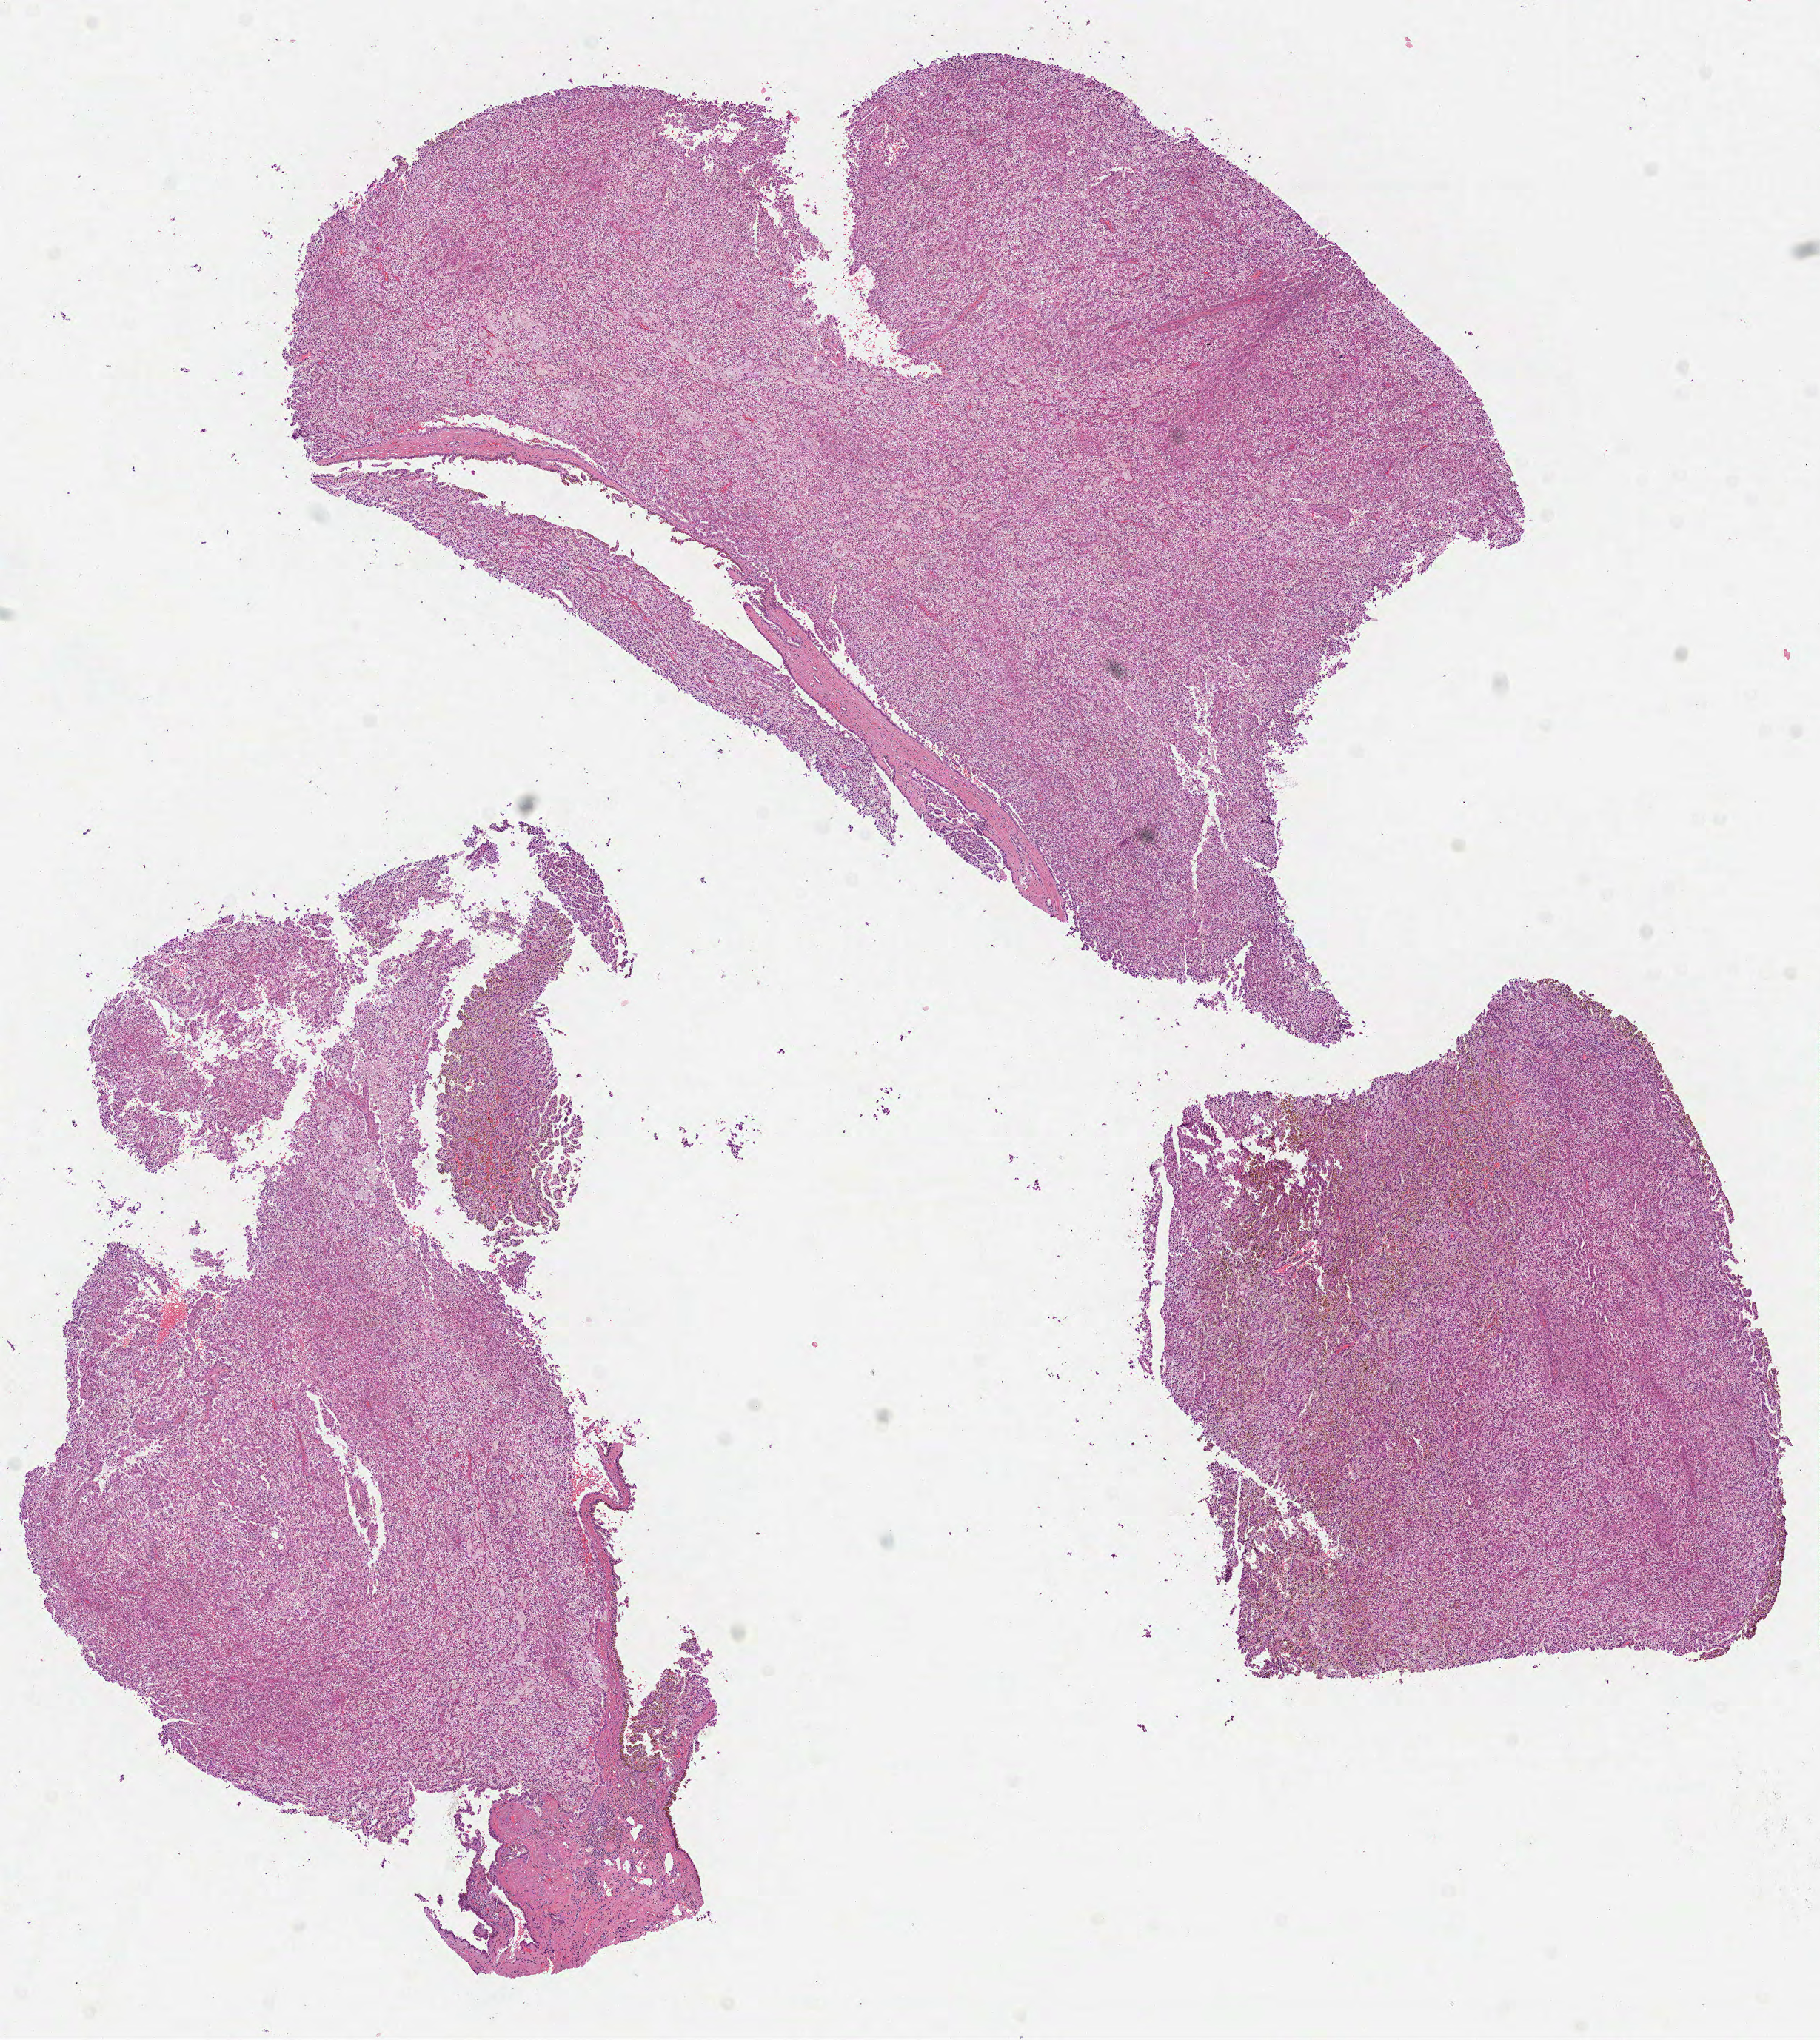
Digitized H&E-stained tissue section (whole slide) — whole scanned area (about 9.9 x 11.1 mm, slide scanned at 40x) shown as a low-resolution overview; formalin-fixed paraffin-embedded (FFPE) diagnostic section; primary tumour sample from the kidney. Patient: male, age at initial diagnosis 50 years. Histologic grade: G2 (moderately differentiated).
TNM: T2 N0 M0. Pathologic diagnosis: Clear cell adenocarcinoma, NOS. AJCC pathologic stage: II.